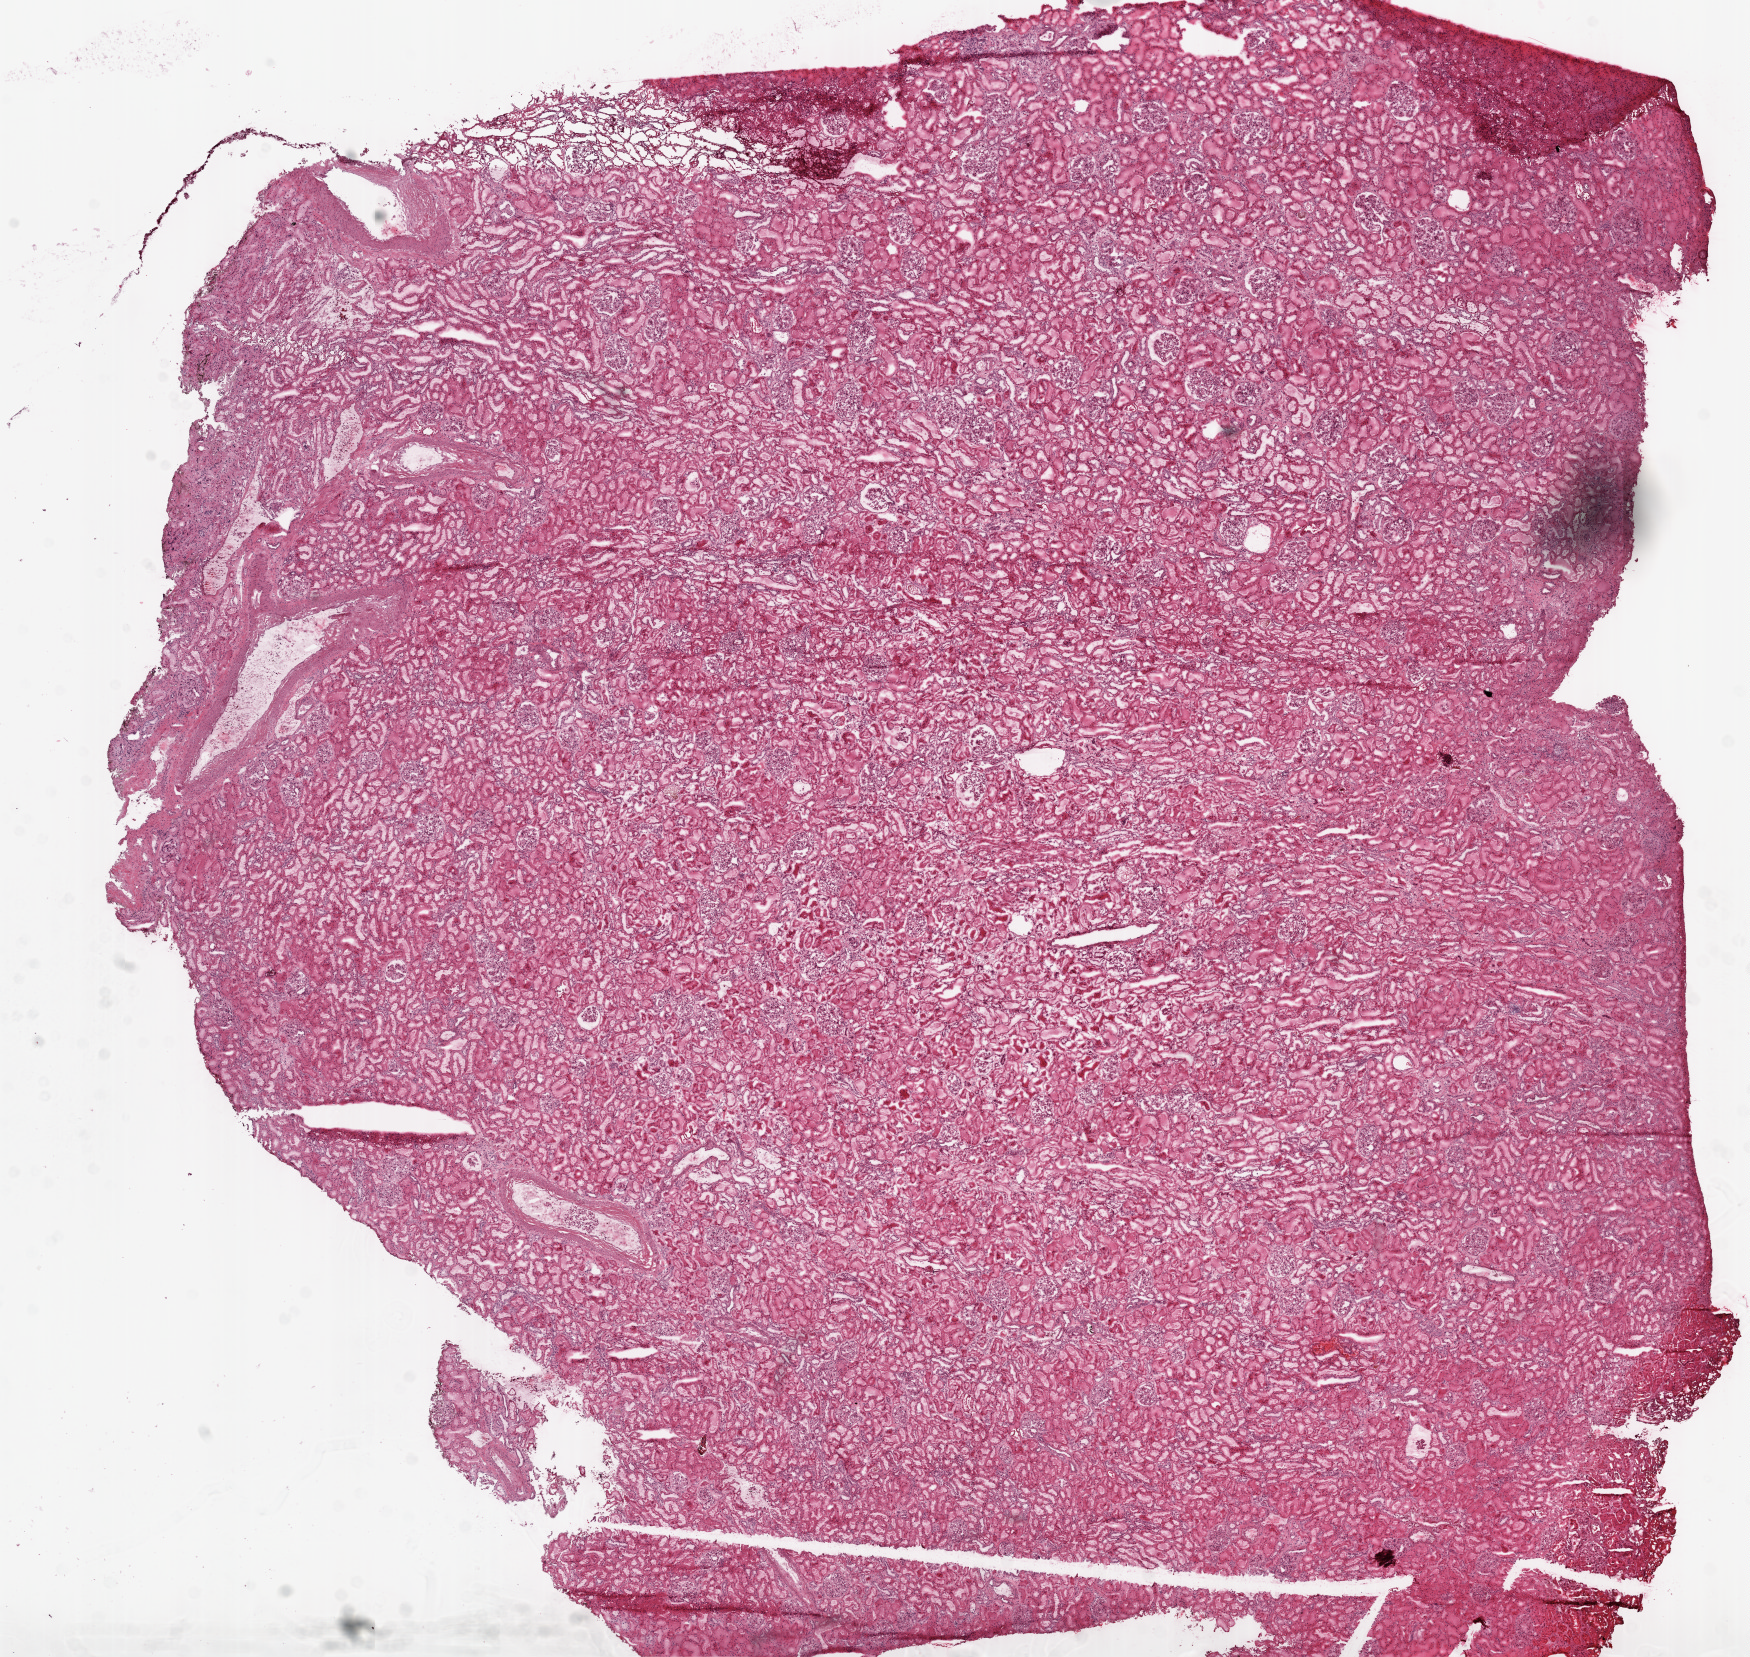
Whole-slide histology image, H&E-stained, shown as a low-resolution overview of the whole scanned area (about 14.0 x 13.3 mm, acquisition: 20x scan), frozen section from the top of the tissue portion, solid tissue normal (non-tumour tissue) sample from the kidney. Patient: male, age at initial diagnosis 53 years.
This section: solid tissue normal (non-tumour) sample from the same patient. Patient diagnosis: Clear cell adenocarcinoma, NOS.